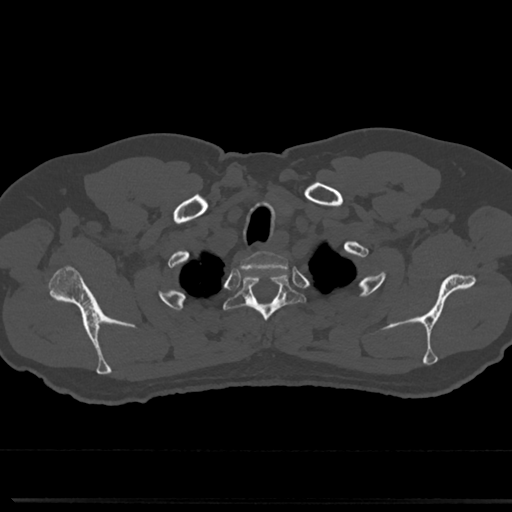
CT including the spine, one axial slice; position 643 of 817 along the scan axis; reconstruction kernel Br40s/3; bone window (W 1800 / L 400 HU); 512 × 512 image matrix. Male patient, age 61 years. From the clinical record (not read from this slice): primary cancer: prostate.
Structures marked on this image (semi-automatic segmentation, software-assisted and operator-edited):
- T1 vertebra: bounding box (x1, y1, x2, y2) in pixels: (251, 253, 282, 261)
- T2 vertebra: (229, 270, 299, 350)